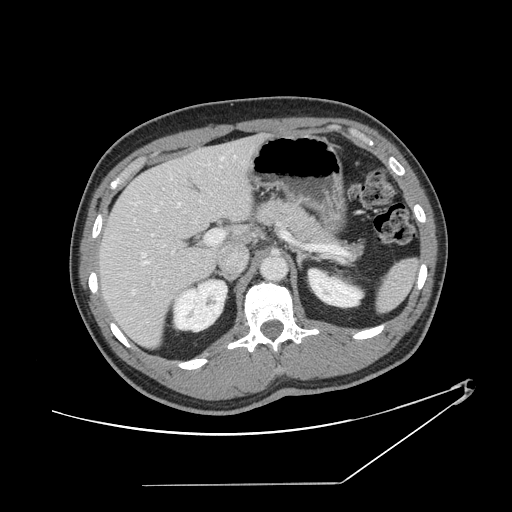
Contrast-enhanced abdominal CT, one axial slice; position 84 of 152 along the scan axis; 120 kVp; soft-tissue window (W 400 / L 40 HU); 2.5 mm slice thickness; 512 × 512 image matrix, field of view 432 × 432 mm. Male patient, age 45 years. From the clinical record (not read from this slice): diagnosis: colorectal cancer liver metastases, imaged before liver resection; multiple liver metastases: no; largest metastasis: 1 cm; disease in both lobes: no.
Structures marked on this image (manually delineated by an expert):
- hepatic veins: box from (x=112, y=156) to (x=225, y=294) px
- liver: (x=100, y=136)–(x=261, y=347)
- planned liver remnant (the part of the liver to remain after resection): (x=100, y=156)–(x=218, y=347)
- portal vein (with intrahepatic branches): (x=142, y=230)–(x=314, y=265)